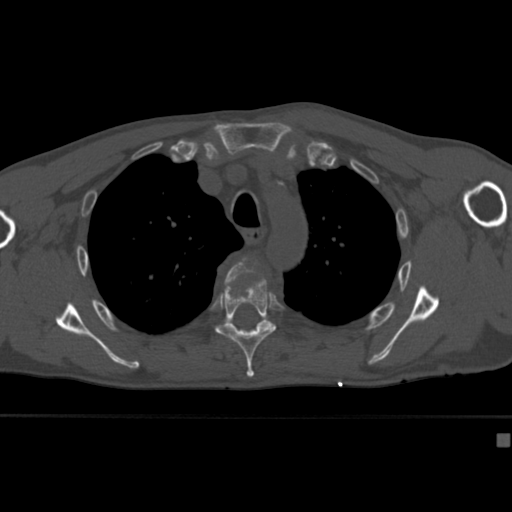
CT including the spine, one axial slice; position 310 of 430 along the scan axis; 120 kVp; bone window (W 1800 / L 400 HU); 512 × 512 image matrix. Patient: male, 64 years. From the clinical record (not read from this slice): primary cancer: uterus.
Structures marked on this image (semi-automatic segmentation, software-assisted and operator-edited):
- T4 vertebra: bounding box <225,257,261,282> (left, top, right, bottom; pixels)
- T5 vertebra: <214,275,277,378>